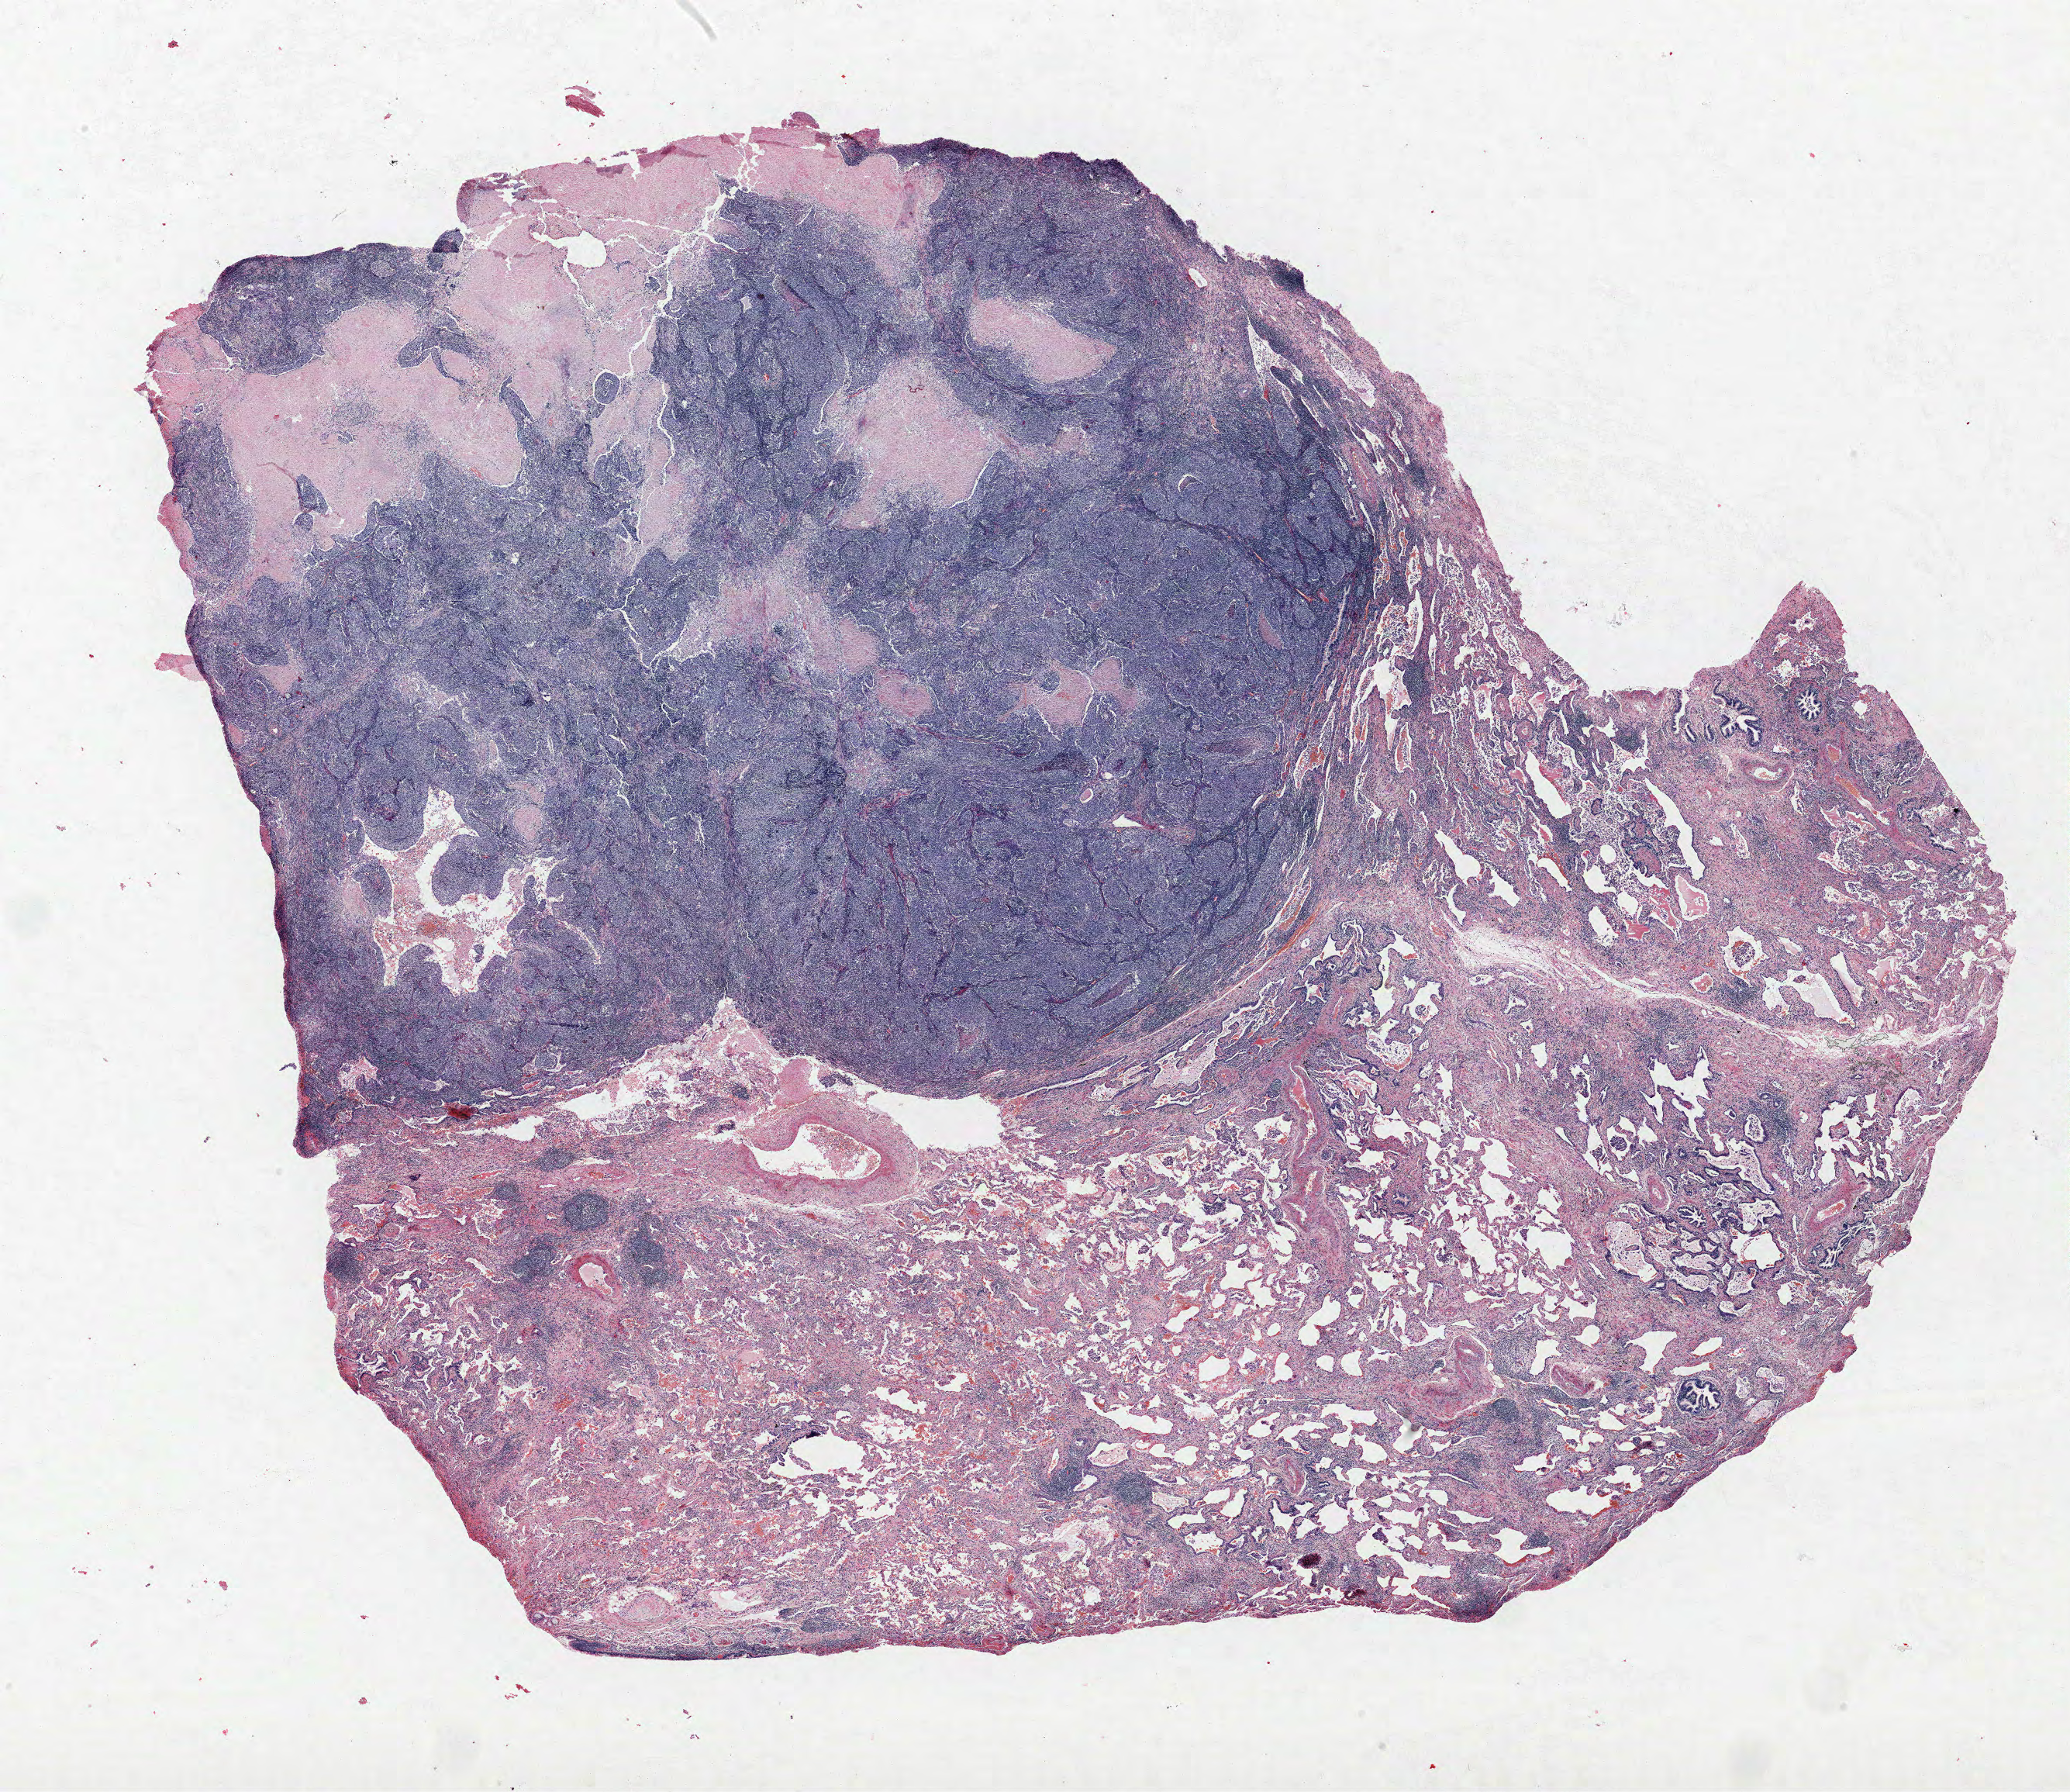
H&E whole-slide image, low-resolution overview of the scanned area, about 21.4 x 18.5 mm; formalin-fixed paraffin-embedded (FFPE) section; lung. Female patient, aged 68 at enrolment. Former smoker at enrolment. Grade: poorly differentiated (G3).
Primary tumour location (clinical record): right lower lobe. Tumour size (pathology): 32 mm. Participant's lung-cancer diagnosis: Large cell carcinoma, NOS (ICD-O-3 8012/3). Stage (AJCC 6th edition): IB.